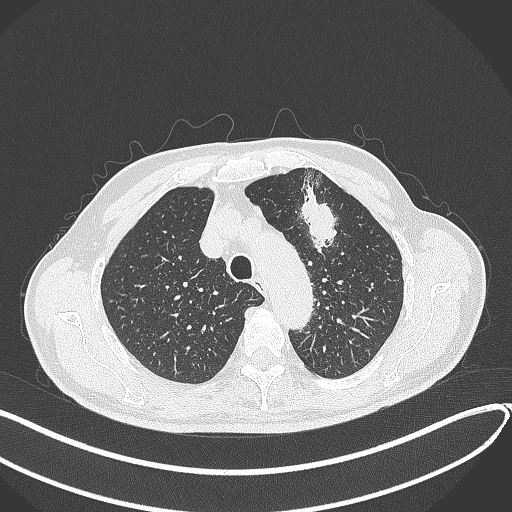
Chest CT, one axial slice; reconstruction kernel B70f; 120 kVp; lung window (W 1500 / L -600 HU); 1 mm slice thickness; 512 × 512 image matrix. Patient: male, 74 years. From the clinical record (not read from this slice): clinical TNM (as recorded): T2b N0 M1c.
Outlined on this slice (rectangle marked by the reading radiologist):
- lung tumour (recorded histology: adenocarcinoma): box from (x=297, y=186) to (x=340, y=261) px